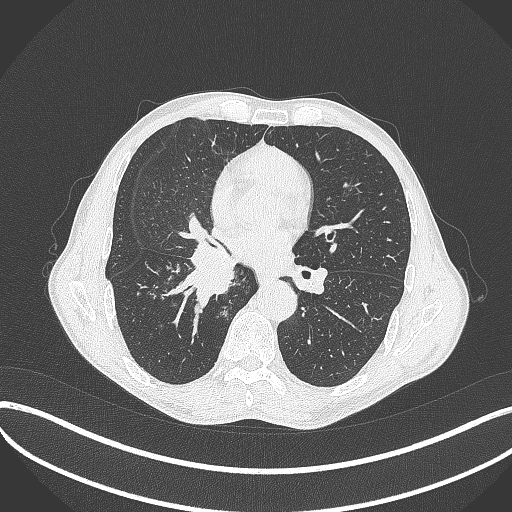
Chest CT, one axial slice. Slice 216 of 481 in the series (ordered by position). Reconstruction kernel B70f. Lung window (W 1500 / L -600 HU). 1 mm slice thickness. 512 × 512 image matrix. Male patient, age 65 years. From the clinical record (not read from this slice): clinical TNM (as recorded): T2a N0 M0.
Outlined on this slice (bounding box drawn by a radiologist):
- lung tumour (recorded histology: squamous cell carcinoma): bounding box (x1, y1, x2, y2) in pixels: (169, 243, 237, 309)